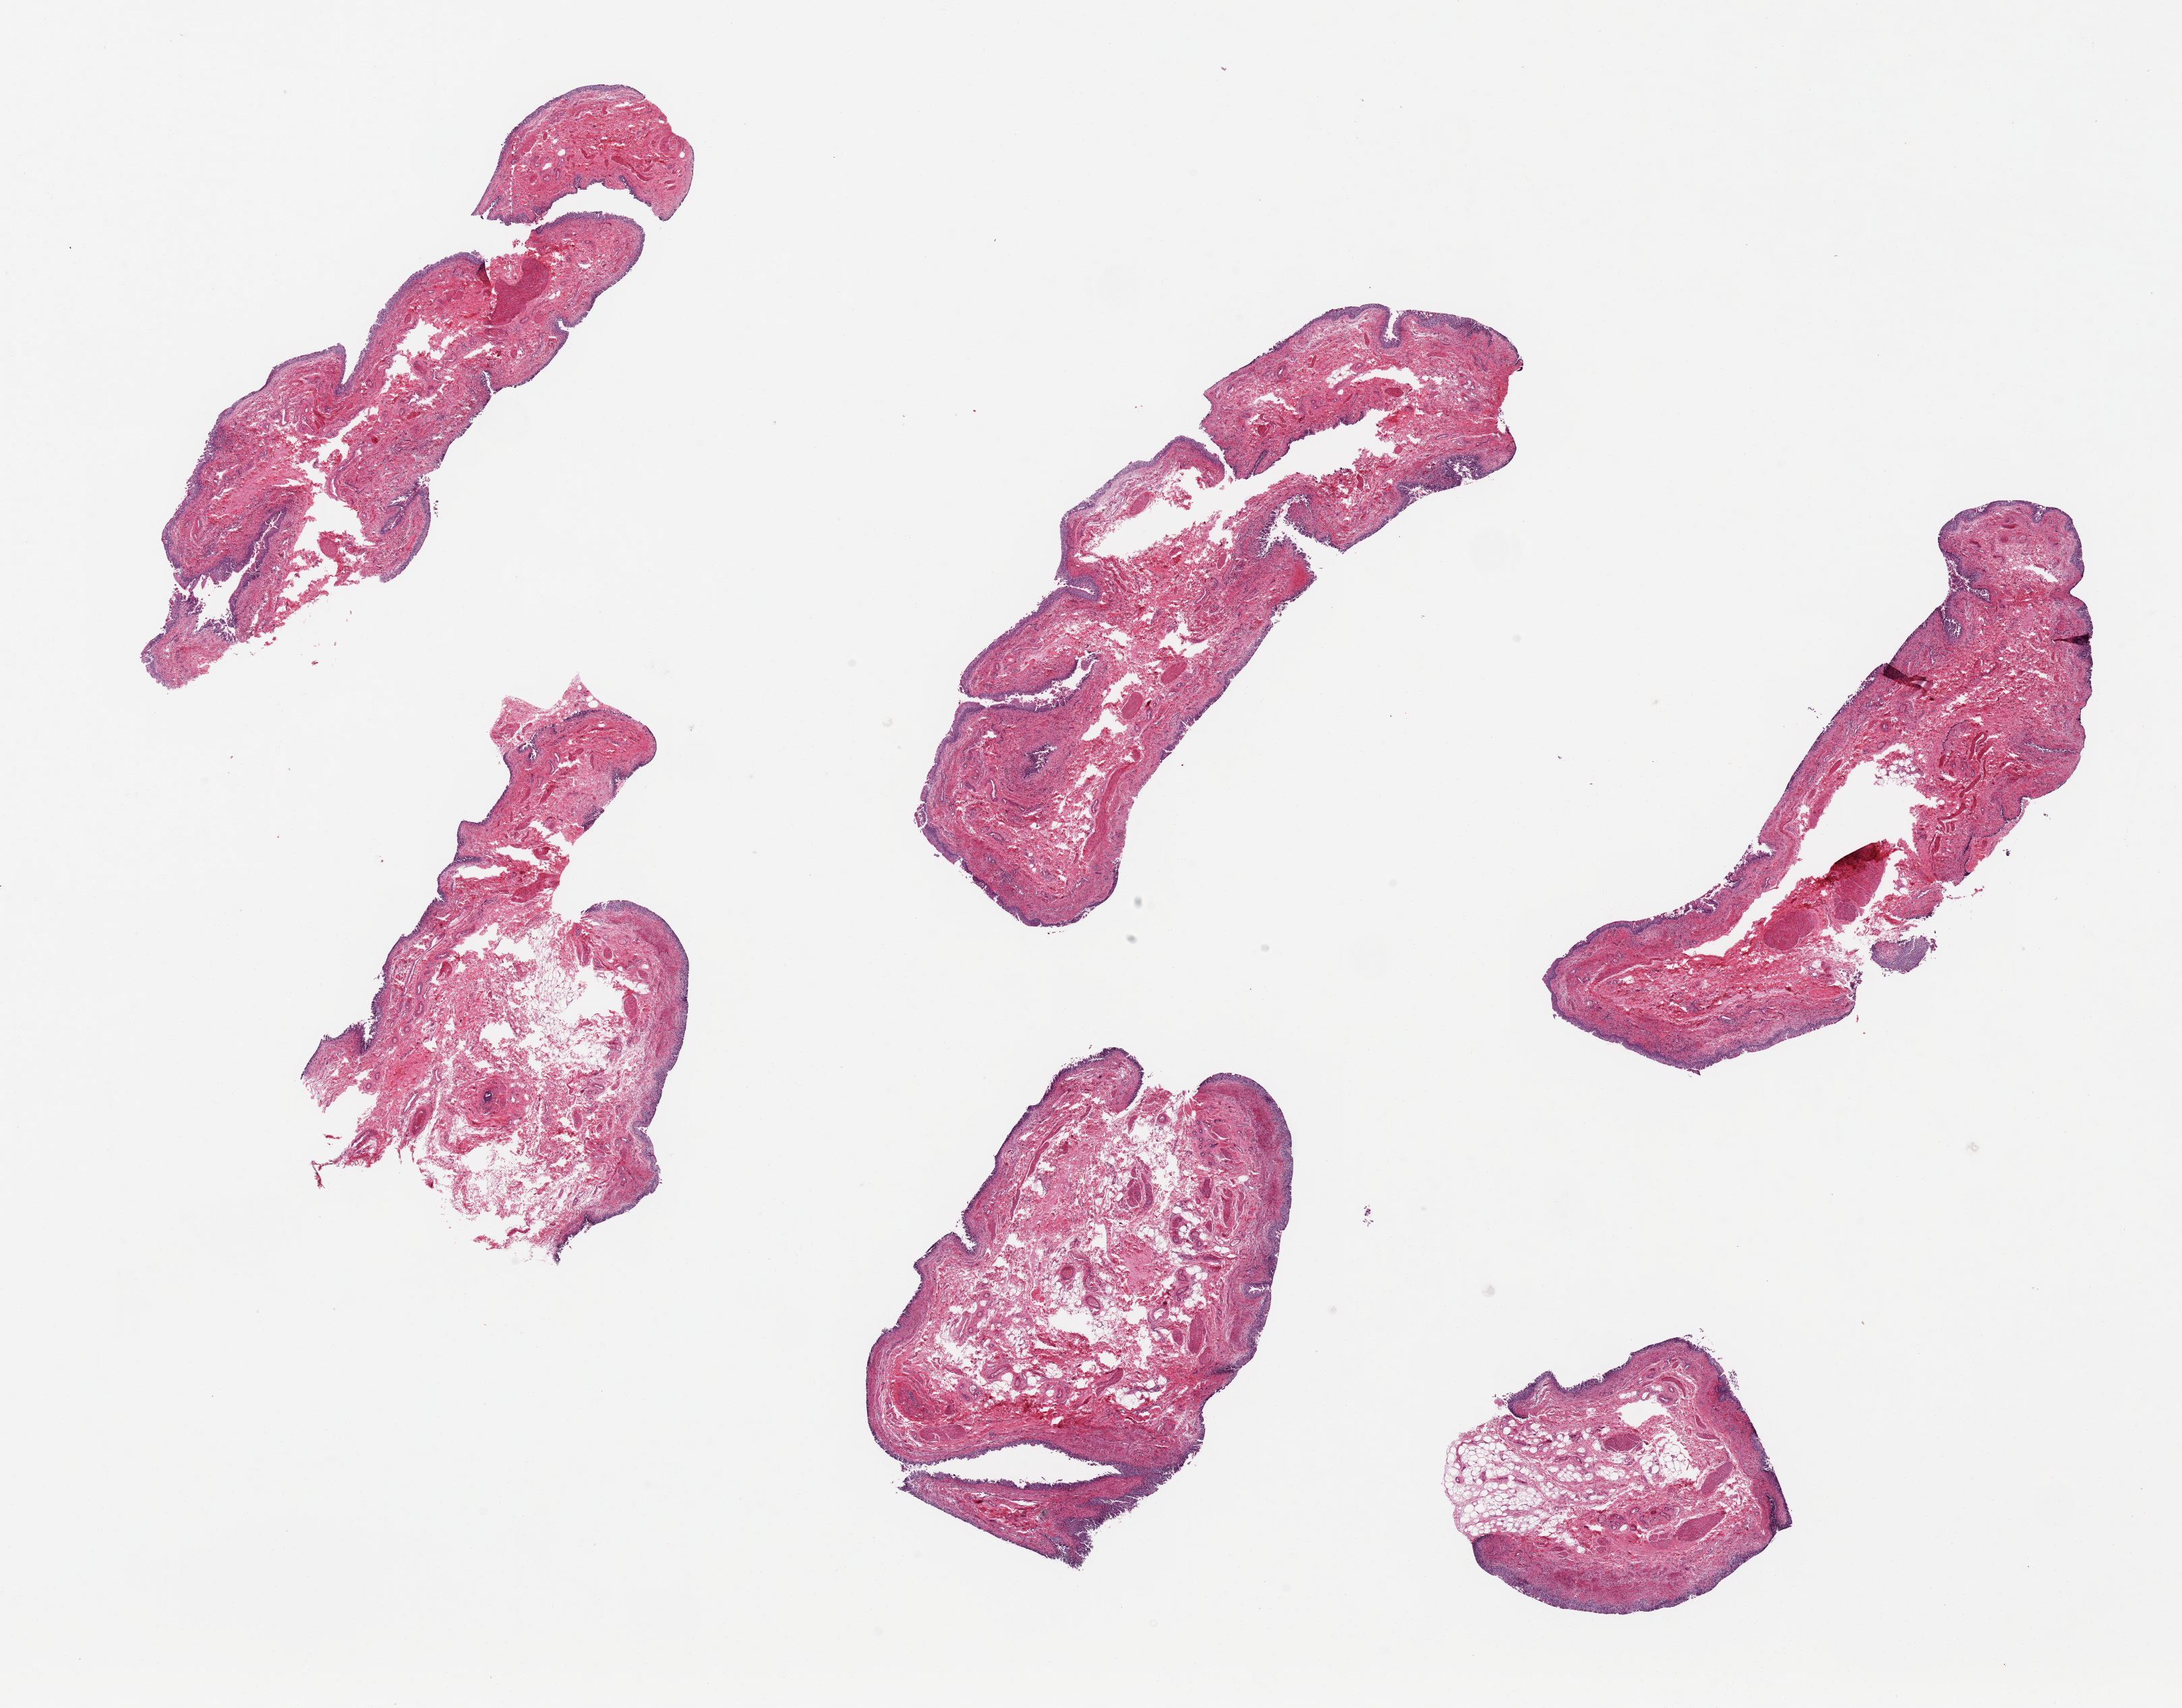
H&E whole-slide image — a low-resolution overview of the entire scanned area, about 25.6 x 20.0 mm, PAXgene-fixed, paraffin-embedded tissue, target tissue: urinary bladder, tissue donor sample. Donor: male.
- pathologist's review note for this sample: 6 pieces, ~9x2mm. Urothelium better preserved than usual, ~3-4% of thickness